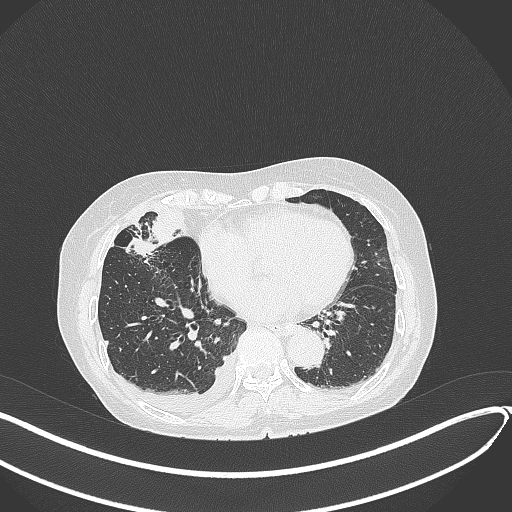
Chest CT, one axial slice. Slice 143 of 418 in the series (ordered by position). Lung window (W 1500 / L -600 HU). 512 × 512 image matrix, field of view 400 × 400 mm. Patient: female, 75 years. From the clinical record (not read from this slice): clinical TNM (as recorded): T2a N3 M0.
Outlined on this slice (bounding box drawn by a radiologist):
- lung tumour (recorded histology: adenocarcinoma): bounding box [x1, y1, x2, y2] px = [120, 230, 159, 261]